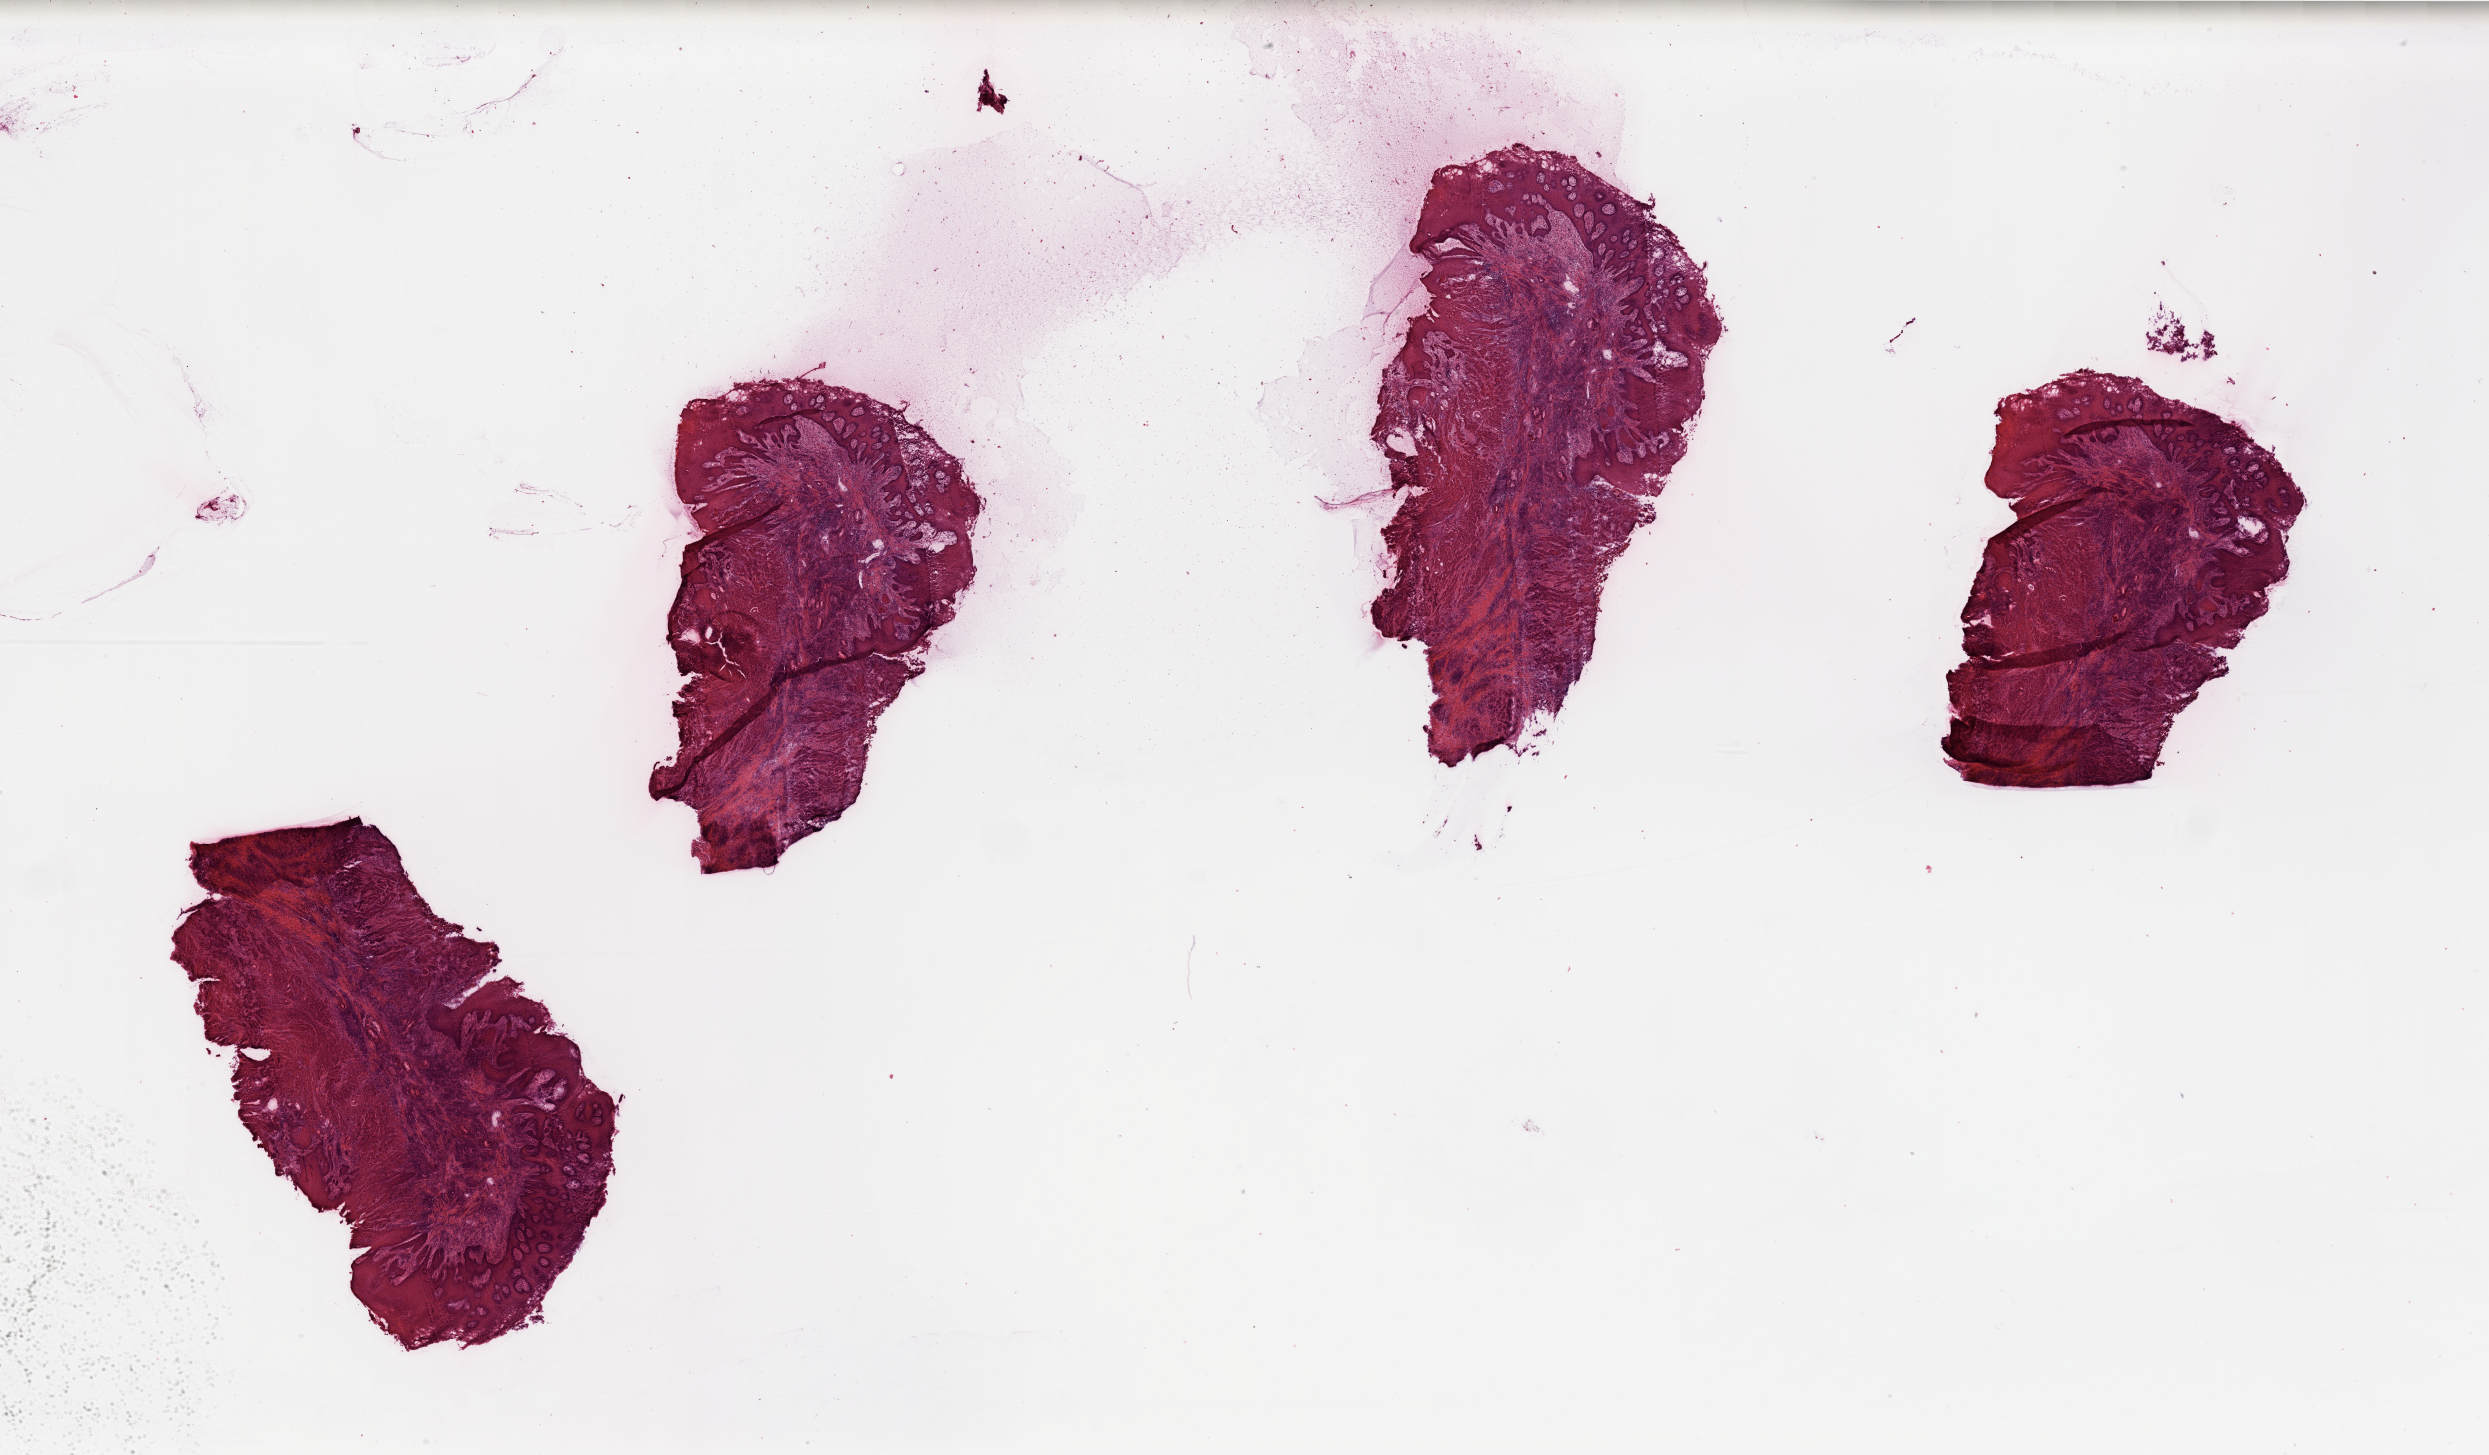
H&E whole-slide image — whole scanned area (about 39.4 x 23.0 mm, acquisition: 20x scan) shown as a low-resolution overview; head and neck, tissue type not recorded. 50-year-old male patient.
- patient diagnosis: Squamous cell carcinoma, NOS